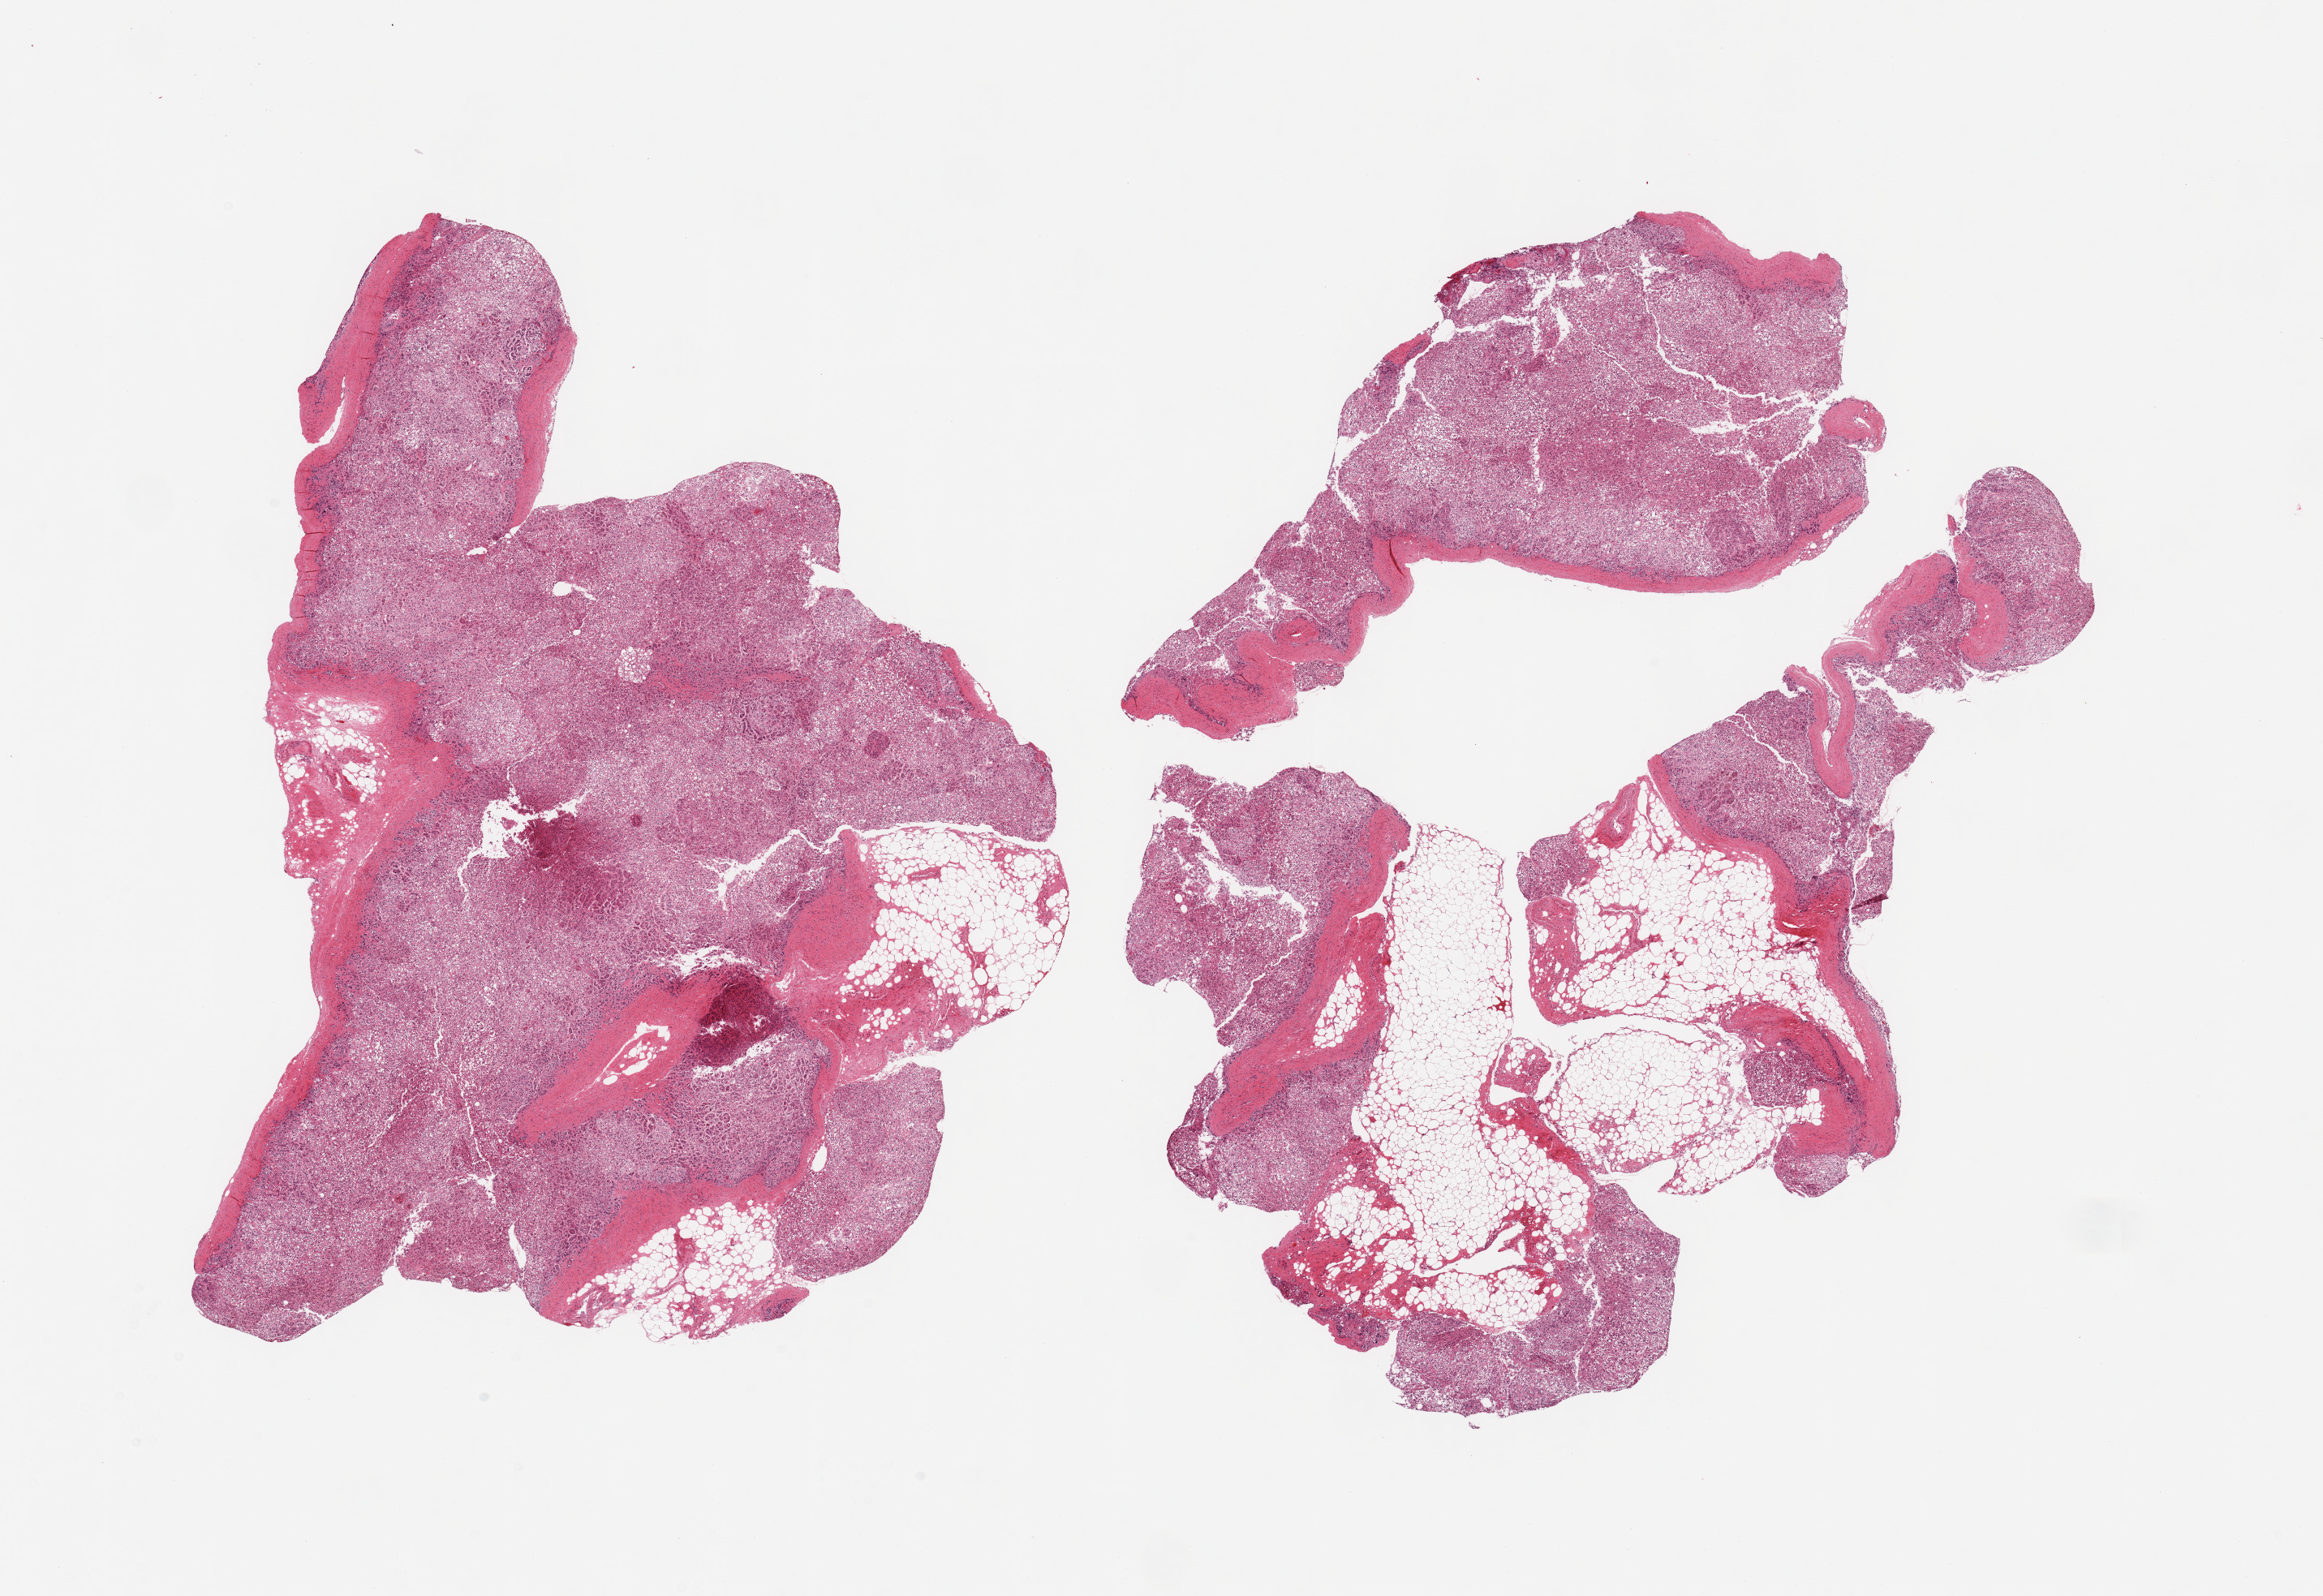
Hematoxylin and eosin (H&E) whole-slide image, low-resolution overview of the scanned area, about 22.6 x 15.6 mm (acquisition: 20x scan). PAXgene-fixed paraffin-embedded (PFPE) section. Target tissue: adrenal gland. Tissue donor sample. Donor: male.
Reviewer comment on this tissue sample: 2 pieces, all cortex.